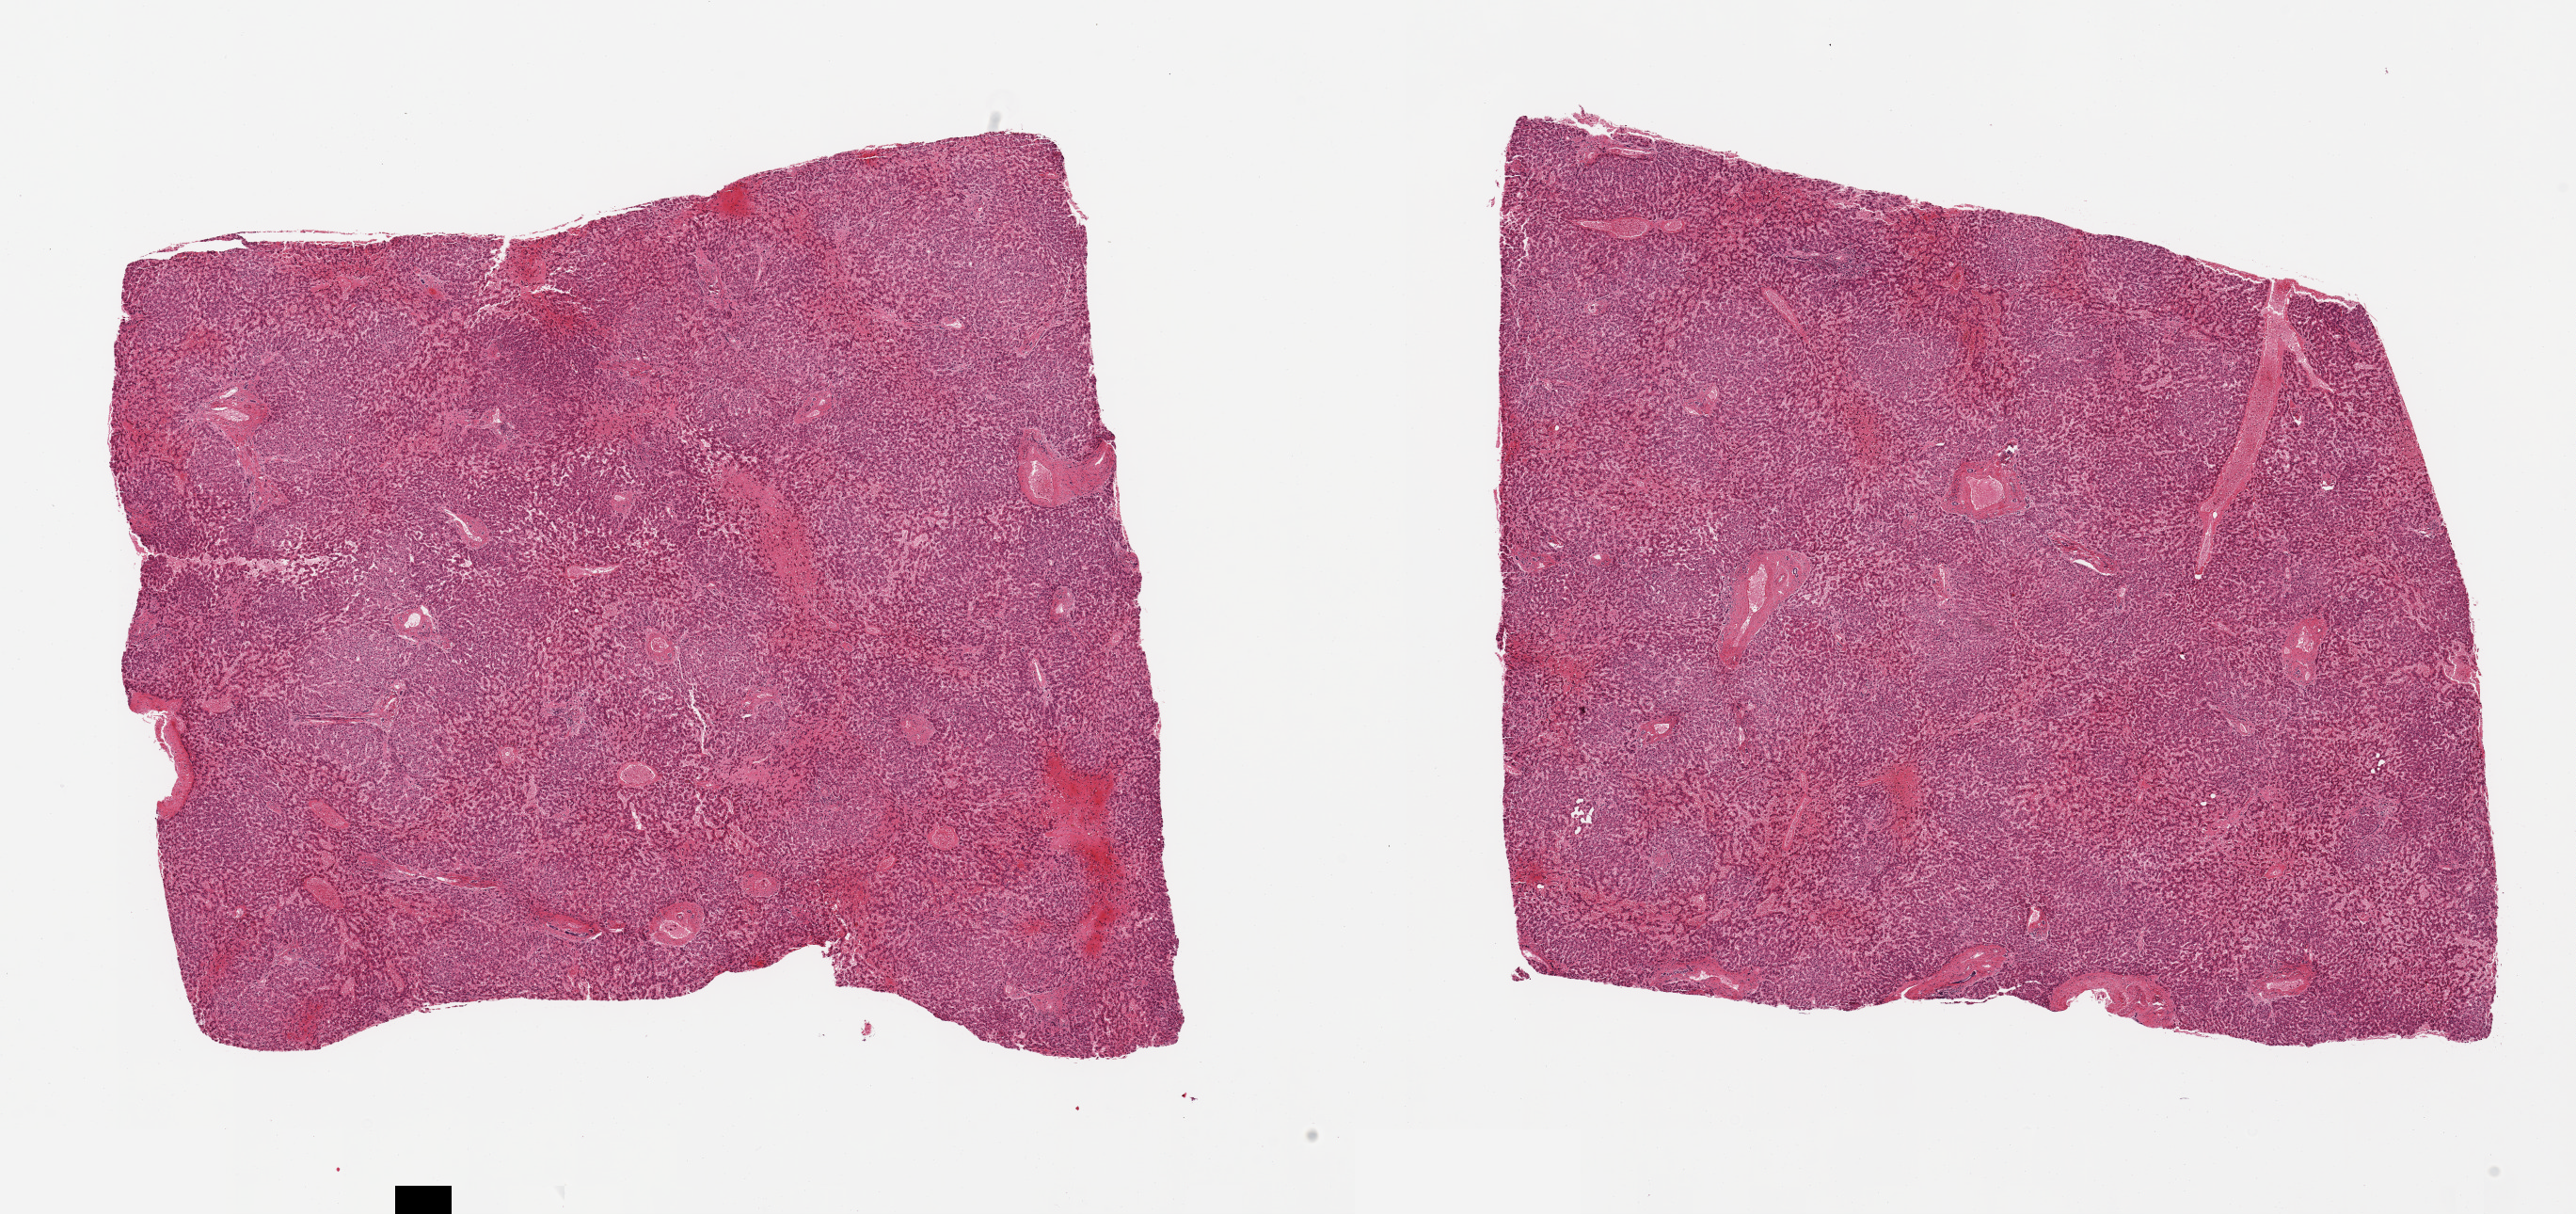
Haematoxylin and eosin whole-slide image, whole scanned area (about 21.7 x 10.2 mm) shown as a low-resolution overview; PAXgene-fixed paraffin-embedded (PFPE) section; section of liver (target tissue); tissue donor sample. Donor sex: male.
Pathologist's review note for this sample: 2 pieces; moderate central congestion, hemorrhage and cellular degeneration consistent with heart failure.